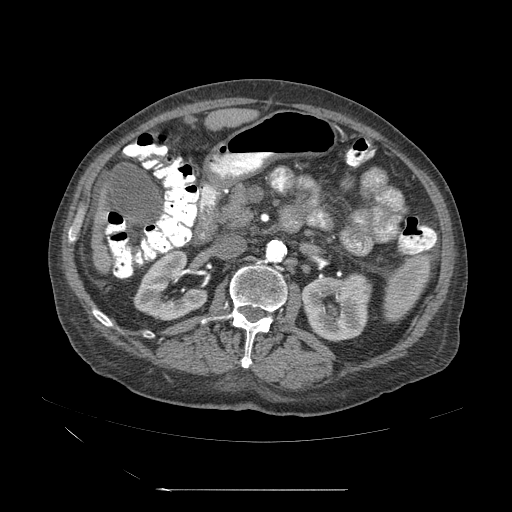
Contrast-enhanced abdominal CT (liver protocol), one axial slice; slice 11 of 71 in the series (ordered by position); 120 kVp; soft-tissue window (W 400 / L 40 HU); 512 × 512 image matrix, field of view 440 × 440 mm. From the clinical record (not read from this slice): diagnosis: hepatocellular carcinoma (patient treated with transarterial chemoembolisation; whether this scan precedes or follows treatment is not stated here); TNM stage (as recorded): Stage-II; Child-Pugh class: A; tumour size: 1 cm.
Outlined on this slice (semi-automatic segmentation, software-assisted and operator-edited):
- abdominal aorta: bounding box <265,241,286,264> (left, top, right, bottom; pixels)